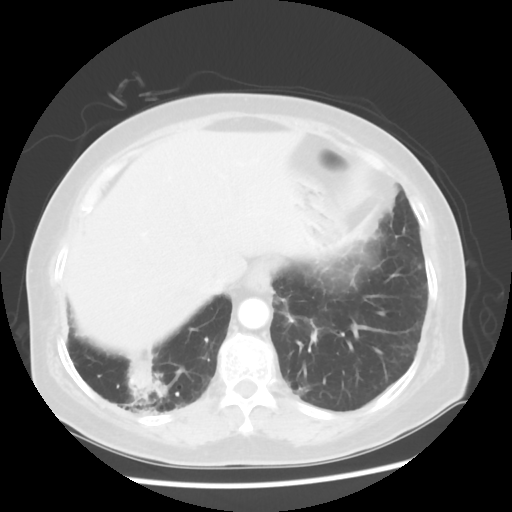
Chest CT, one axial slice. Slice 13 of 56 in the series (ordered by position). 120 kVp. Lung window (W 1500 / L -600 HU). 5 mm slice thickness. 512 × 512 image matrix, field of view 360 × 360 mm. Patient: female, 64 years. Case-level facts recorded for this patient, not image findings: clinical TNM (as recorded): Tis N0 M0.
Outlined on this slice (bounding box drawn by a radiologist):
- lung tumour (recorded histology: adenocarcinoma): bounding box <122,346,181,430> (left, top, right, bottom; pixels)